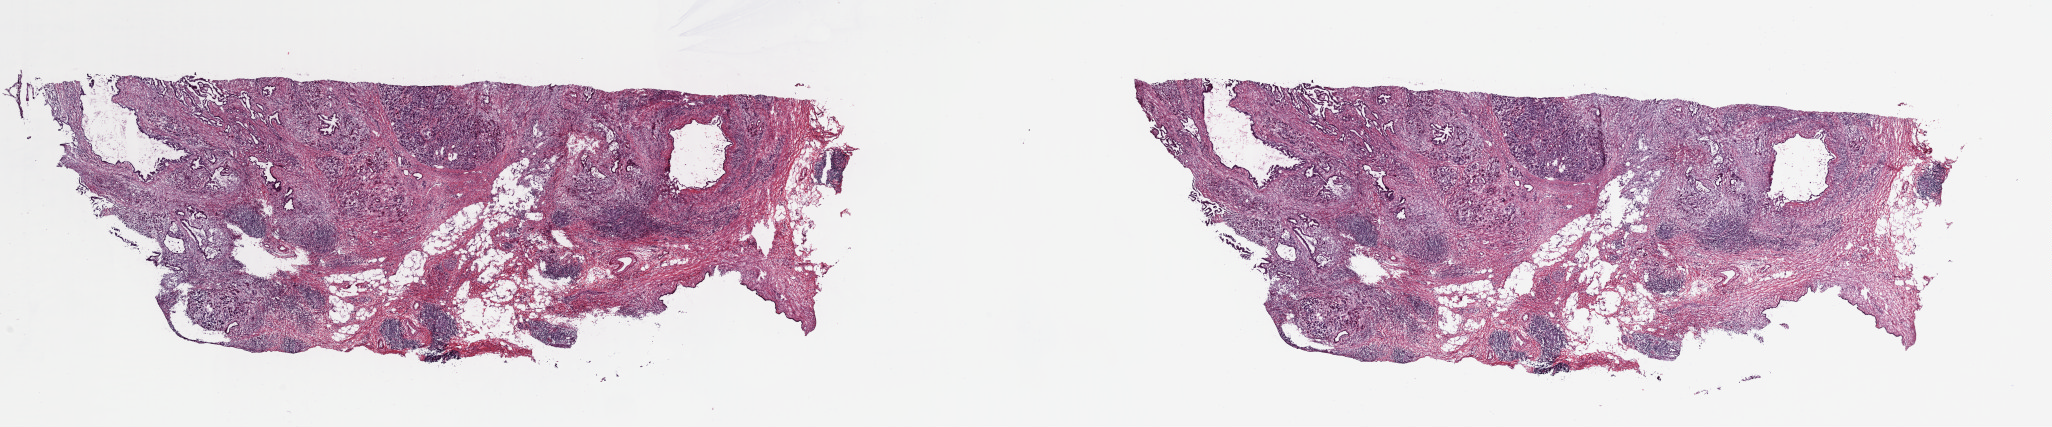
Digitized Hematoxylin and eosin (H&E) stained tissue section (whole slide), whole scanned area (about 32.4 x 6.7 mm, slide scanned at 40x) shown as a low-resolution overview; frozen section from the top of the tissue portion; sample: primary tumour, pancreas. Patient: female, age at initial diagnosis 69 years. Histologic grade: G2 (moderately differentiated). Composition of this section per pathologist review: tumour cells 30%, tumour nuclei 40%, normal cells 20%, stromal cells 50%, necrosis 0%. Inflammatory infiltration, as recorded: lymphocyte infiltration 100%, monocyte infiltration 0%, neutrophil infiltration 0%.
AJCC pathologic stage: IIB (7th edition). TNM: T3 N1 MX. Pathologic diagnosis: Infiltrating duct carcinoma, NOS (head of pancreas). Lymph nodes positive (case pathology): 4 of 40 examined.